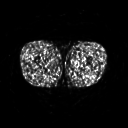
FDG PET of an extremity soft-tissue mass (from a PET/CT study), one axial slice; position 224 of 267 along the scan axis; 128 × 128 image matrix, field of view 500 × 500 mm. Patient: male, 27 years. From the clinical record (not read from this slice): histological type: extraskeletal osteosarcoma; grade: high; site of the primary tumour: left adductur.
Structures marked on this image (expert contour drawn on MRI and transferred to this co-registered scan by the dataset authors):
- gross tumour volume (mass): bounding box [x1, y1, x2, y2] px = [70, 62, 92, 76]